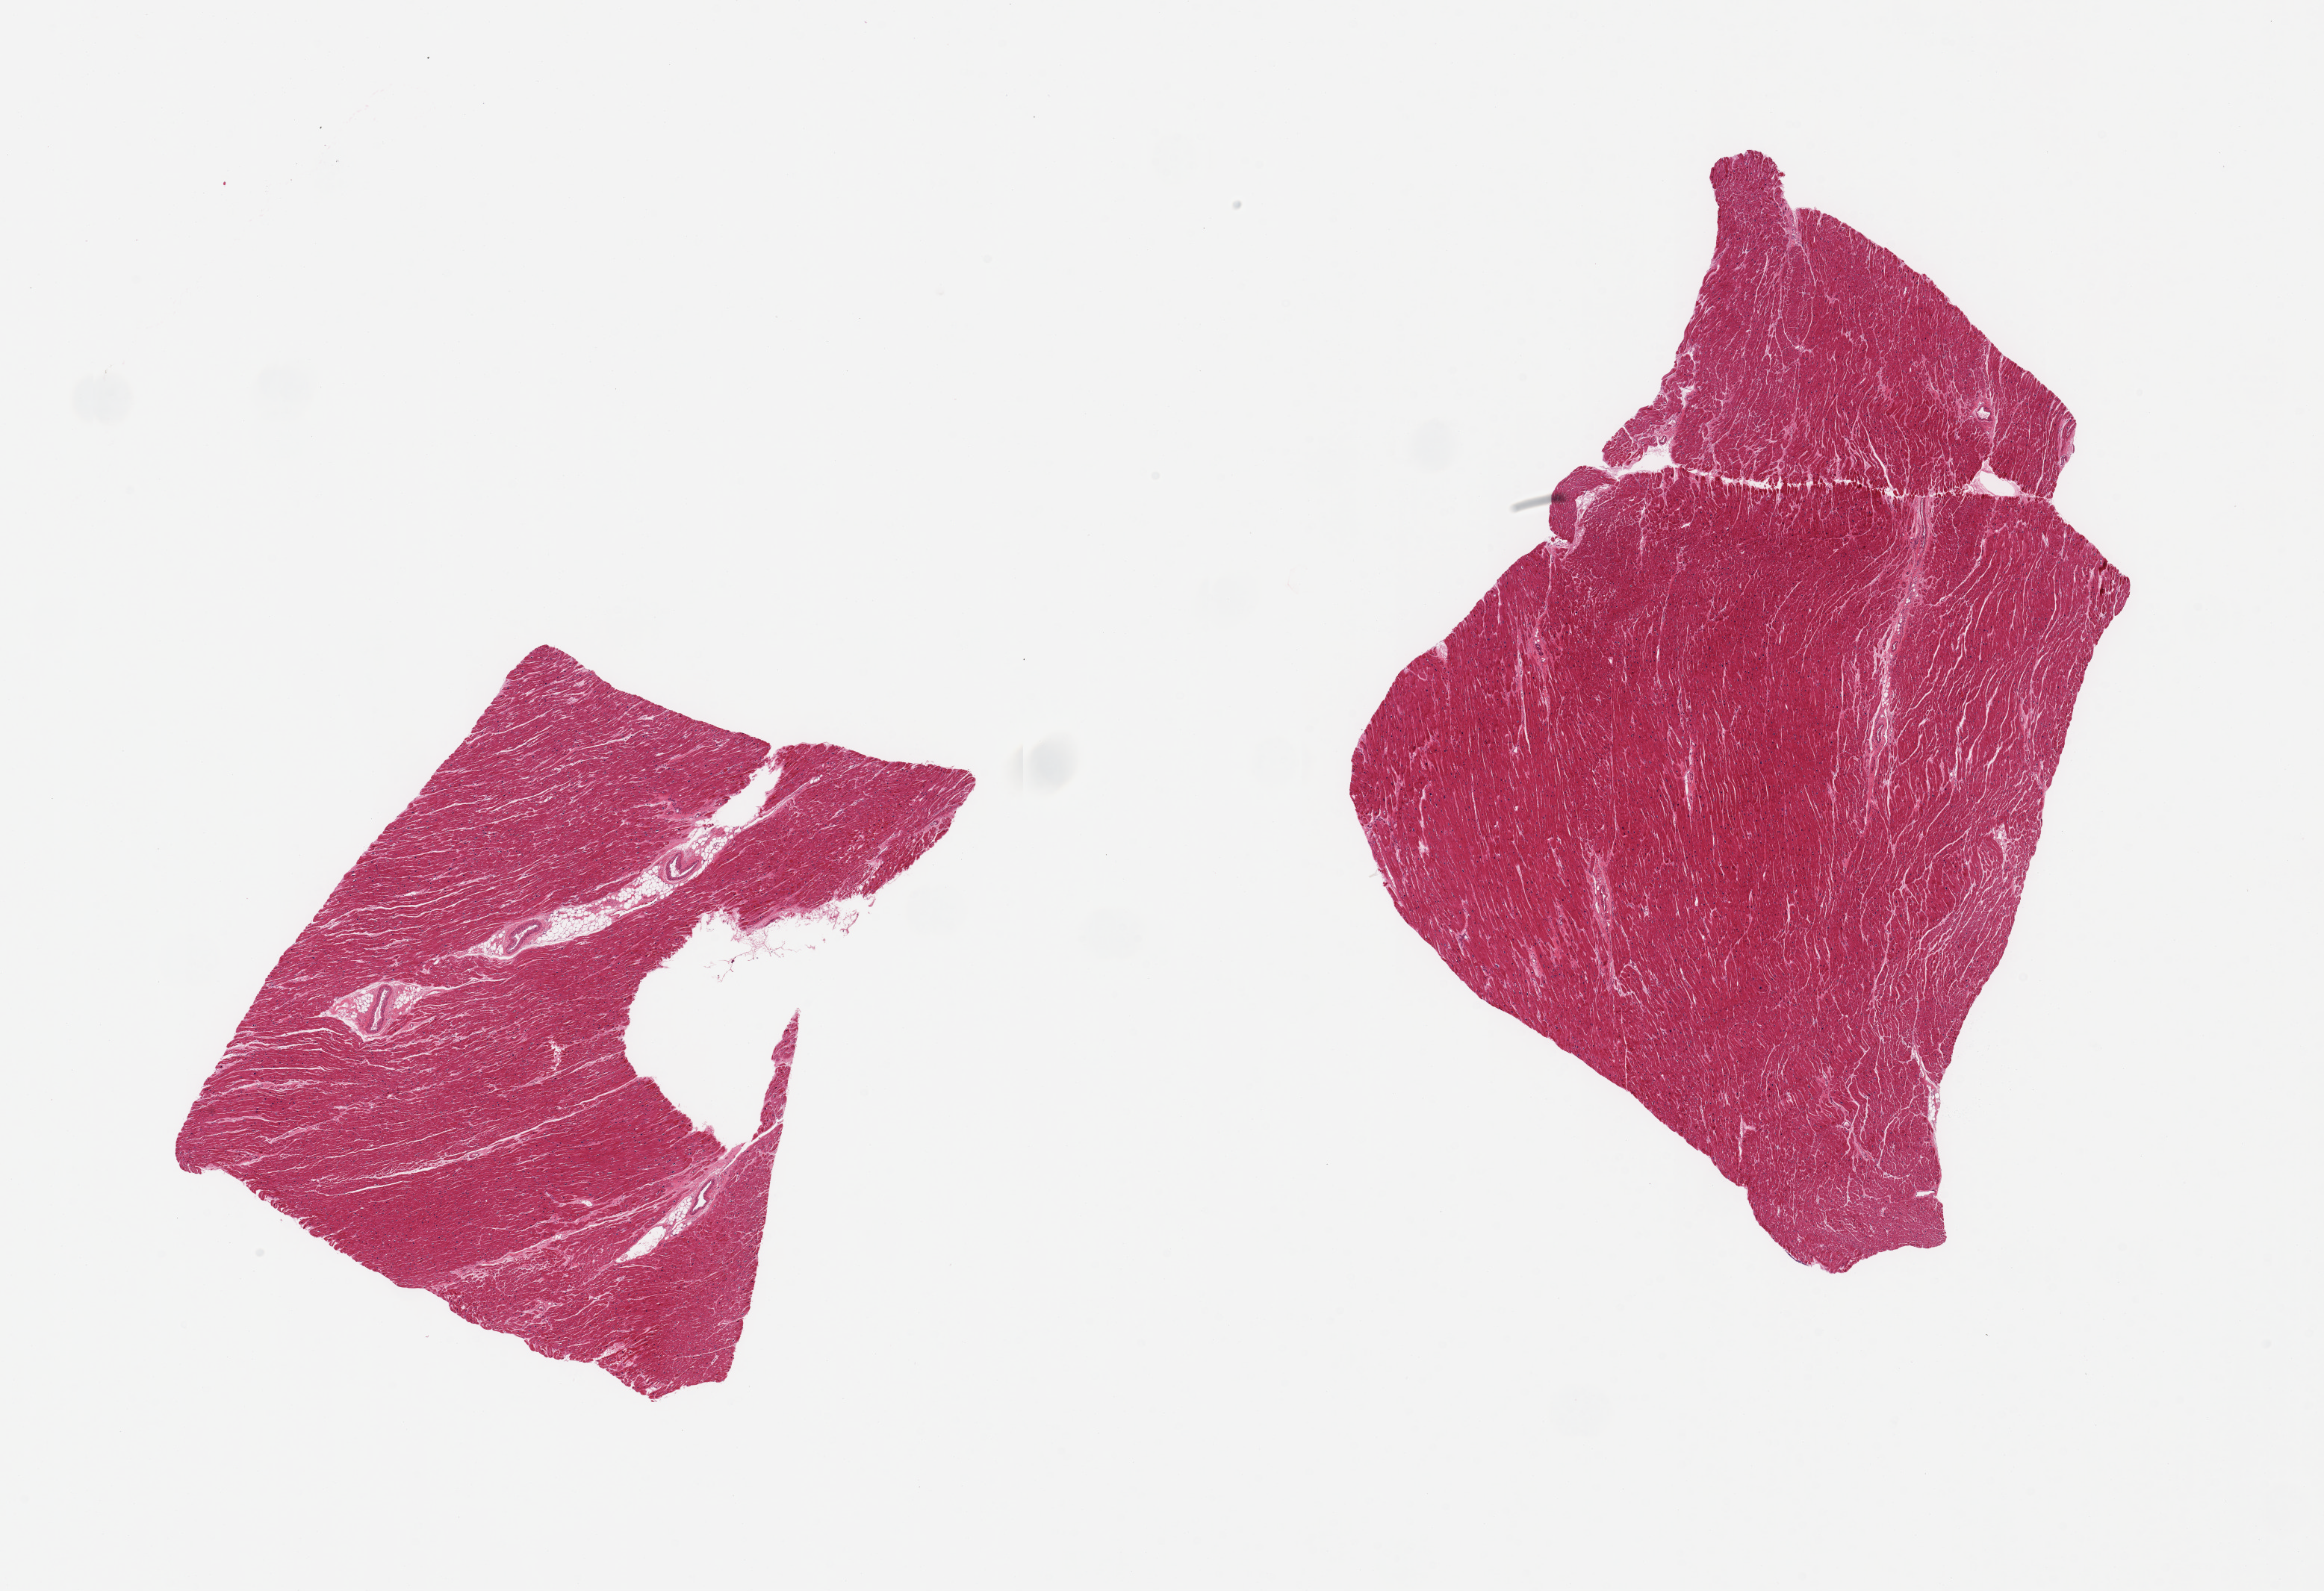
Whole-slide image, hematoxylin and eosin (H&E) stain — a low-resolution overview of the entire scanned area, about 24.6 x 16.9 mm (slide scanned at 20x), PAXgene-fixed paraffin-embedded (PFPE) section, target tissue: heart, tissue donor sample.
• reviewer comment on this tissue sample: 2 pieces; enlarged, distorted nuclei consistent with hypertrophy